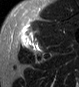
MRI of an extremity soft-tissue mass, one axial slice. Slice 37 of 45 in the series (ordered by position). STIR. MR volume resampled by the dataset authors to the PET/CT grid (not the native acquisition matrix). 3.27 mm slice thickness. 79 × 87 image matrix. Male patient. Case-level facts recorded for this patient, not image findings: histological type: pleiomorphic leiomyosarcoma; grade: high; site of the primary tumour: left thigh.
Structures marked on this image (expert contour drawn on MRI and transferred to this co-registered scan by the dataset authors):
- gross tumour volume including surrounding oedema: bounding box <20,27,42,53> (left, top, right, bottom; pixels)